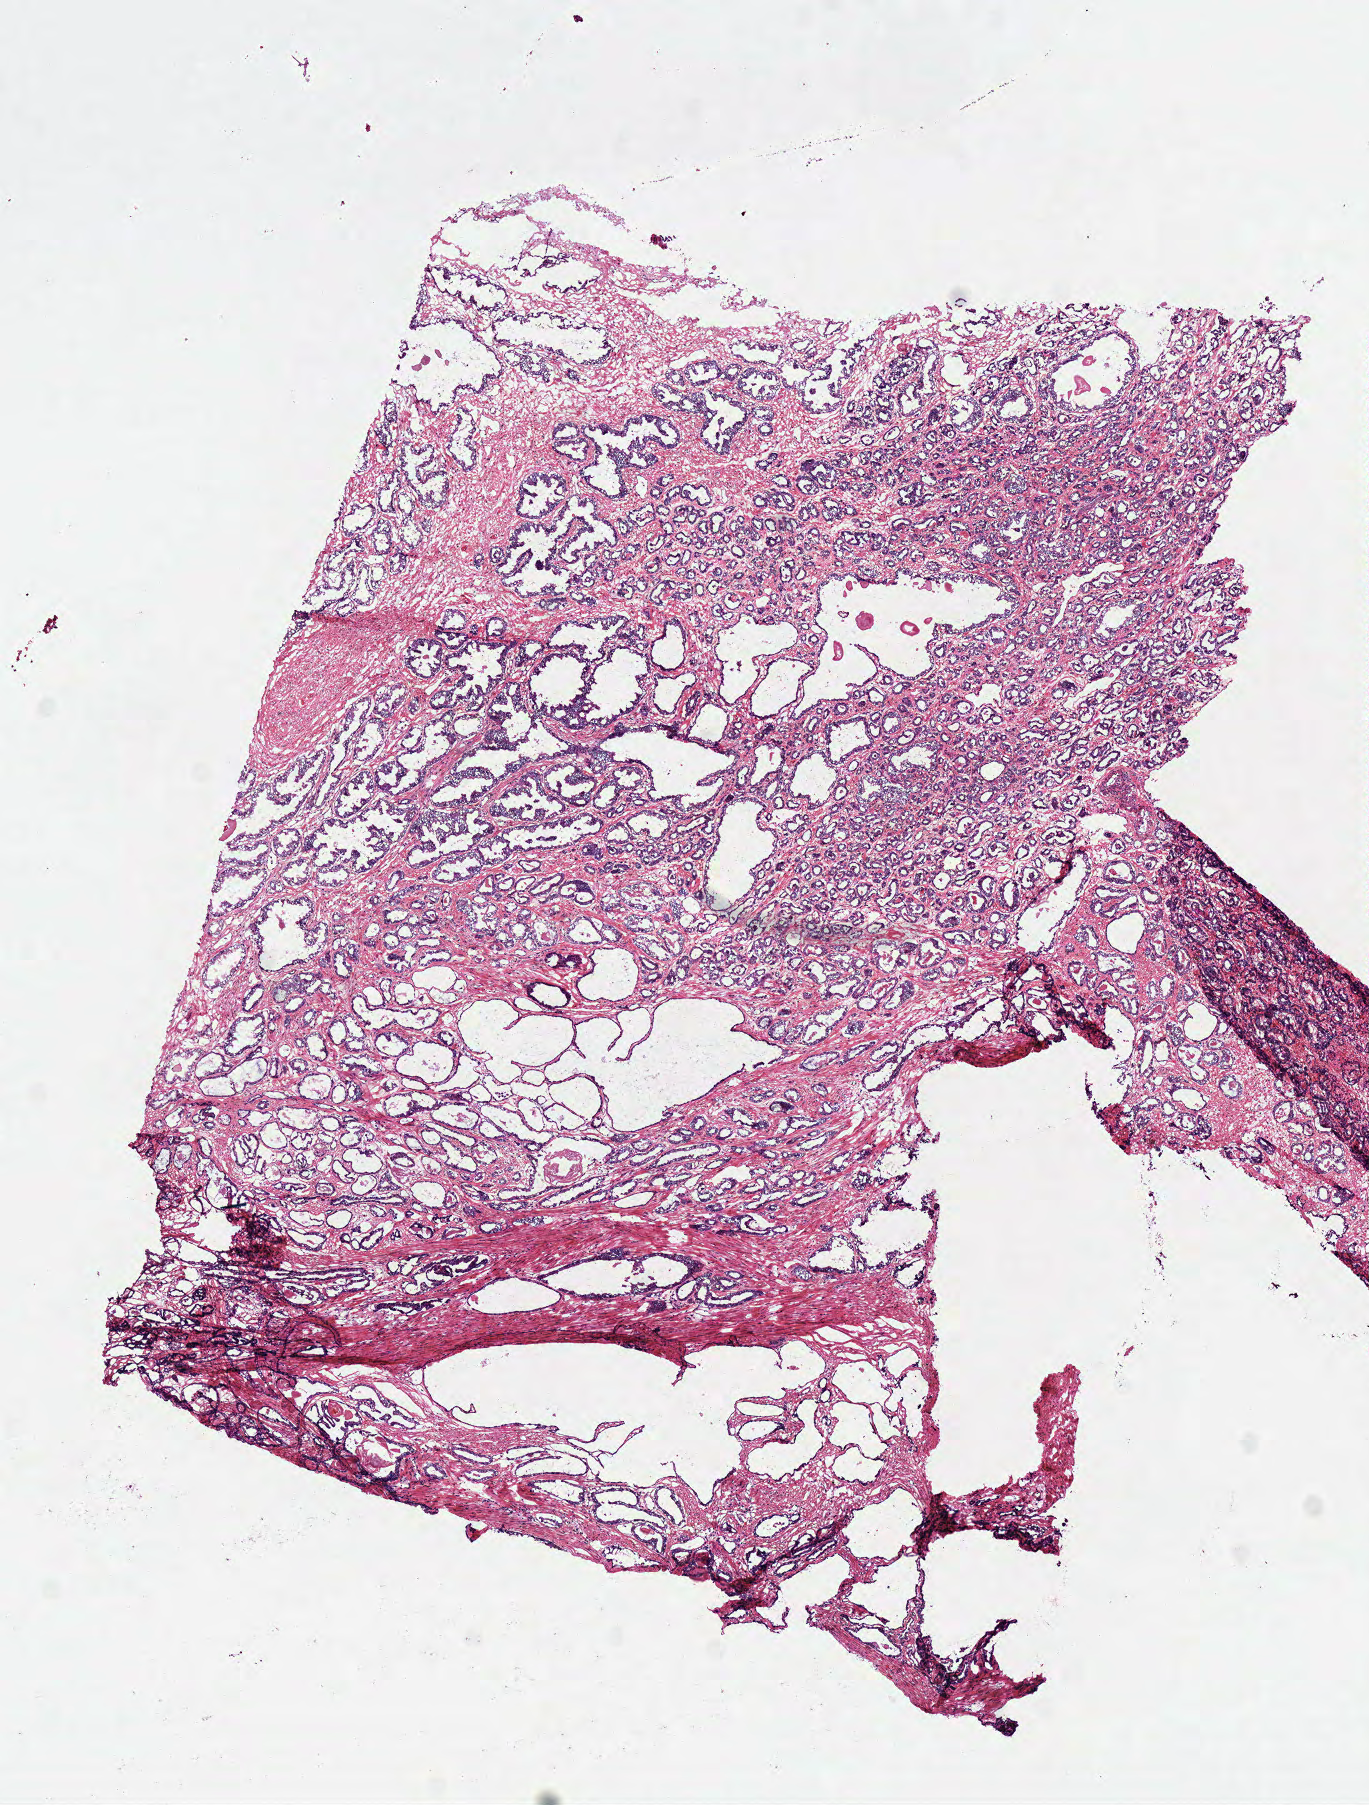
Whole-slide histology image, H&E-stained — whole scanned area (about 5.4 x 7.1 mm) shown as a low-resolution overview, frozen section from the top of the tissue portion, primary tumour sample from the prostate. Male, age 66 years at initial diagnosis. Gleason score: 7 (3+4). Composition of this section per pathologist review: tumour cells 60%, tumour nuclei 60%, normal cells 20%, stromal cells 20%, necrosis 0%. Infiltration values recorded for this section: lymphocyte infiltration 2%, monocyte infiltration 0%, neutrophil infiltration 0%.
Histologic diagnosis: Acinar cell carcinoma (prostate gland).